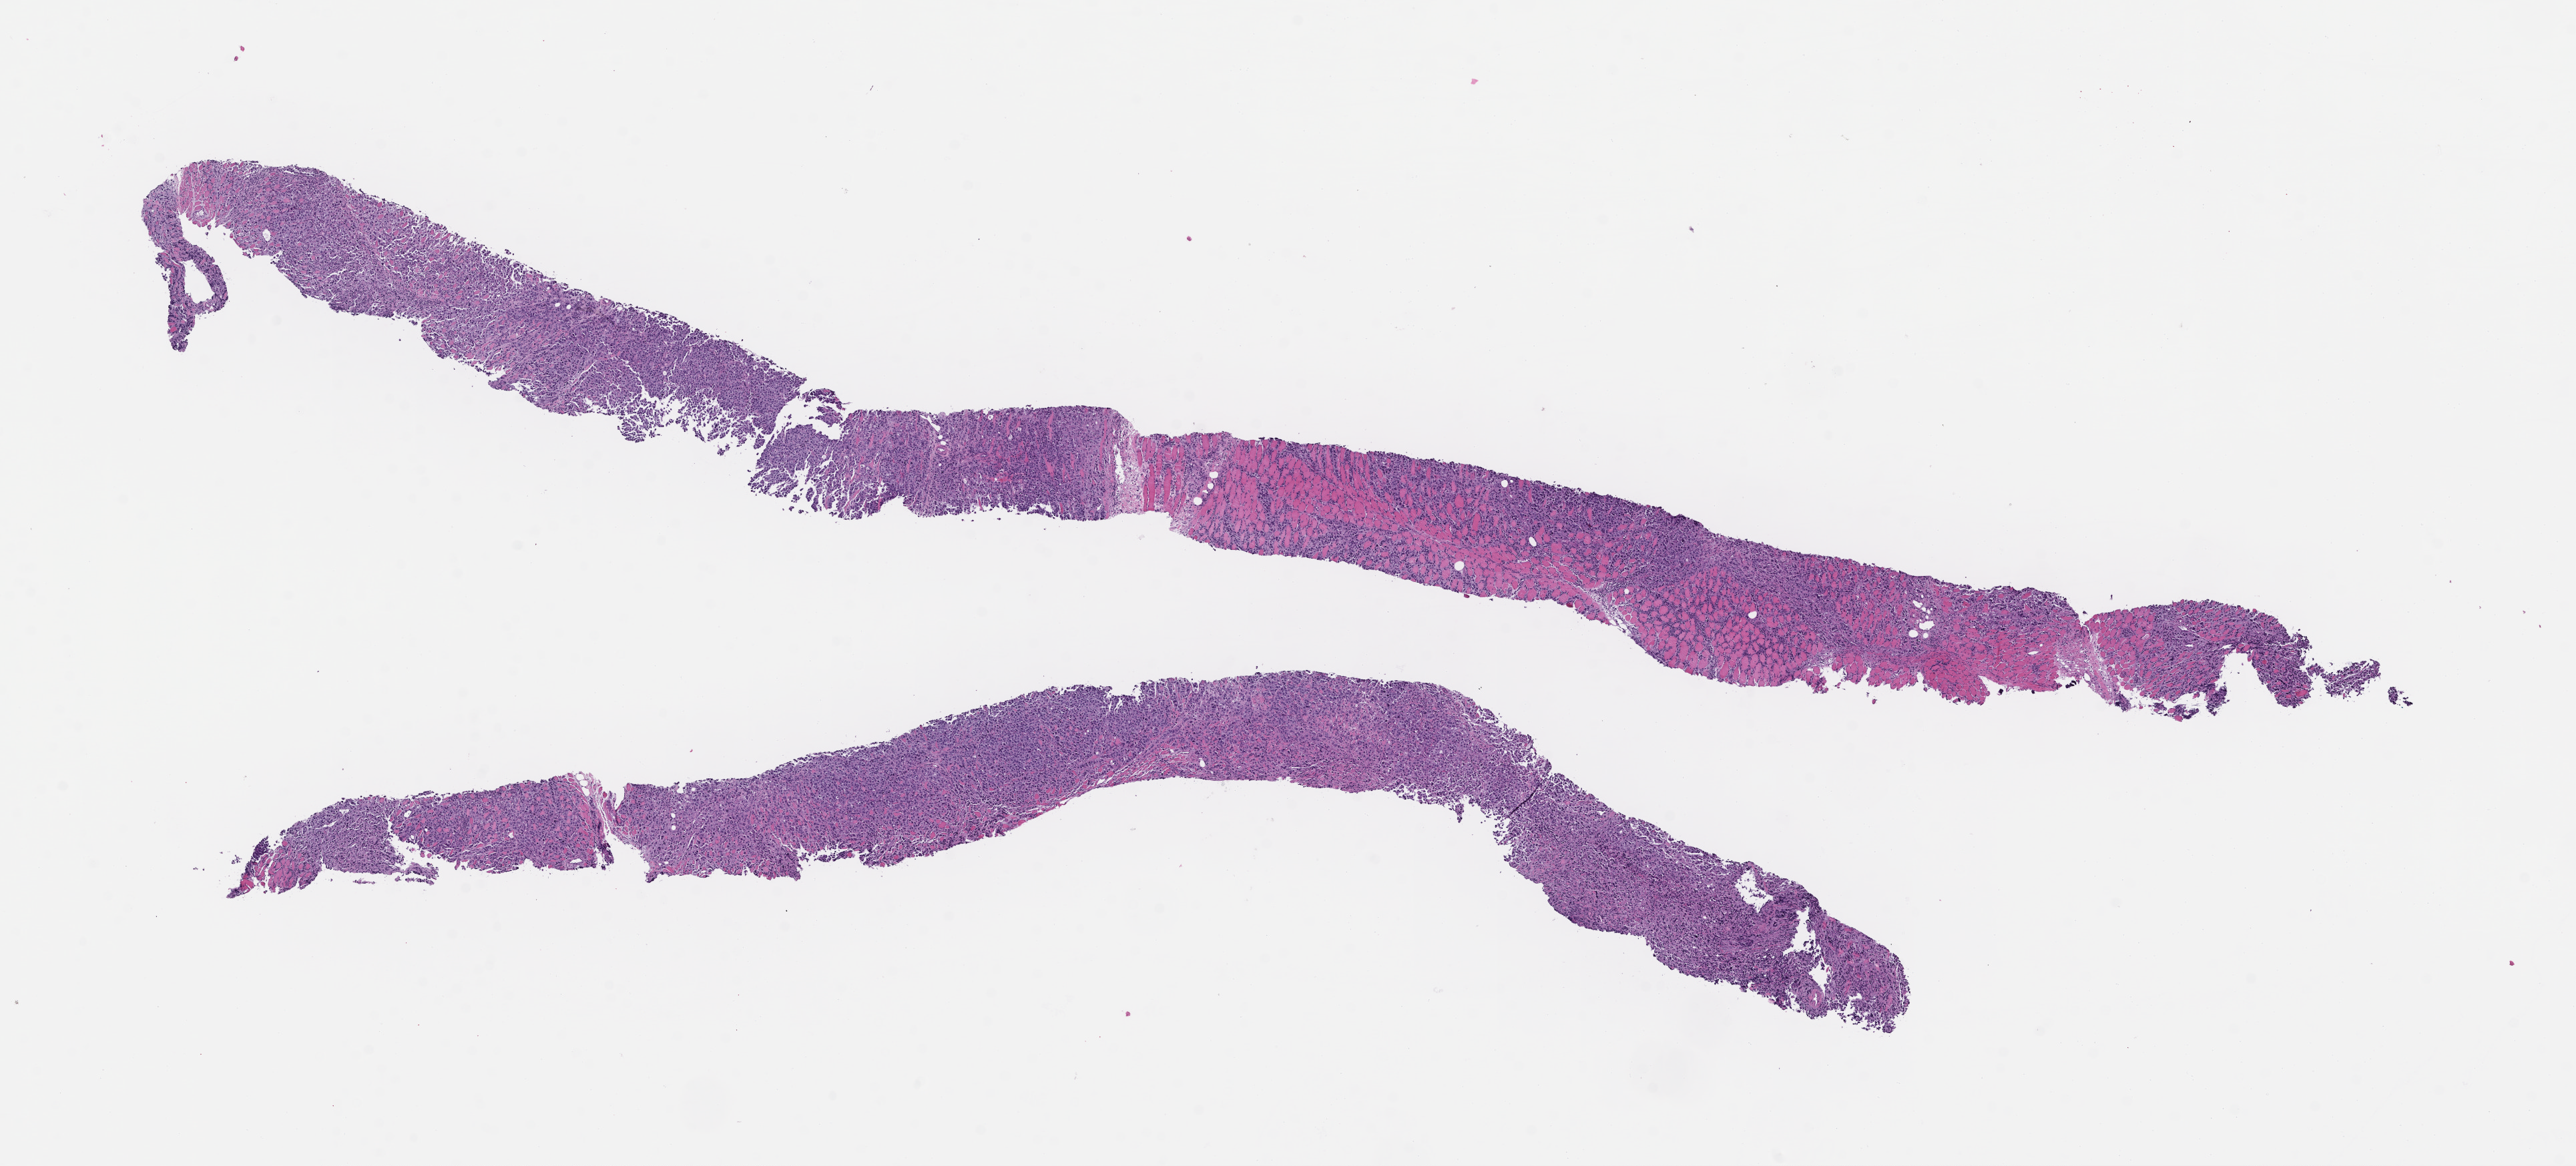
Hematoxylin and eosin (H&E) whole-slide image — a low-resolution overview of the entire scanned area, about 15.6 x 7.1 mm. Formalin-fixed, paraffin-embedded (FFPE) tissue. Archival tissue. Patient: female.
- this section: metastatic tumor tissue
- patient diagnosis (primary): Invasive Breast Carcinoma